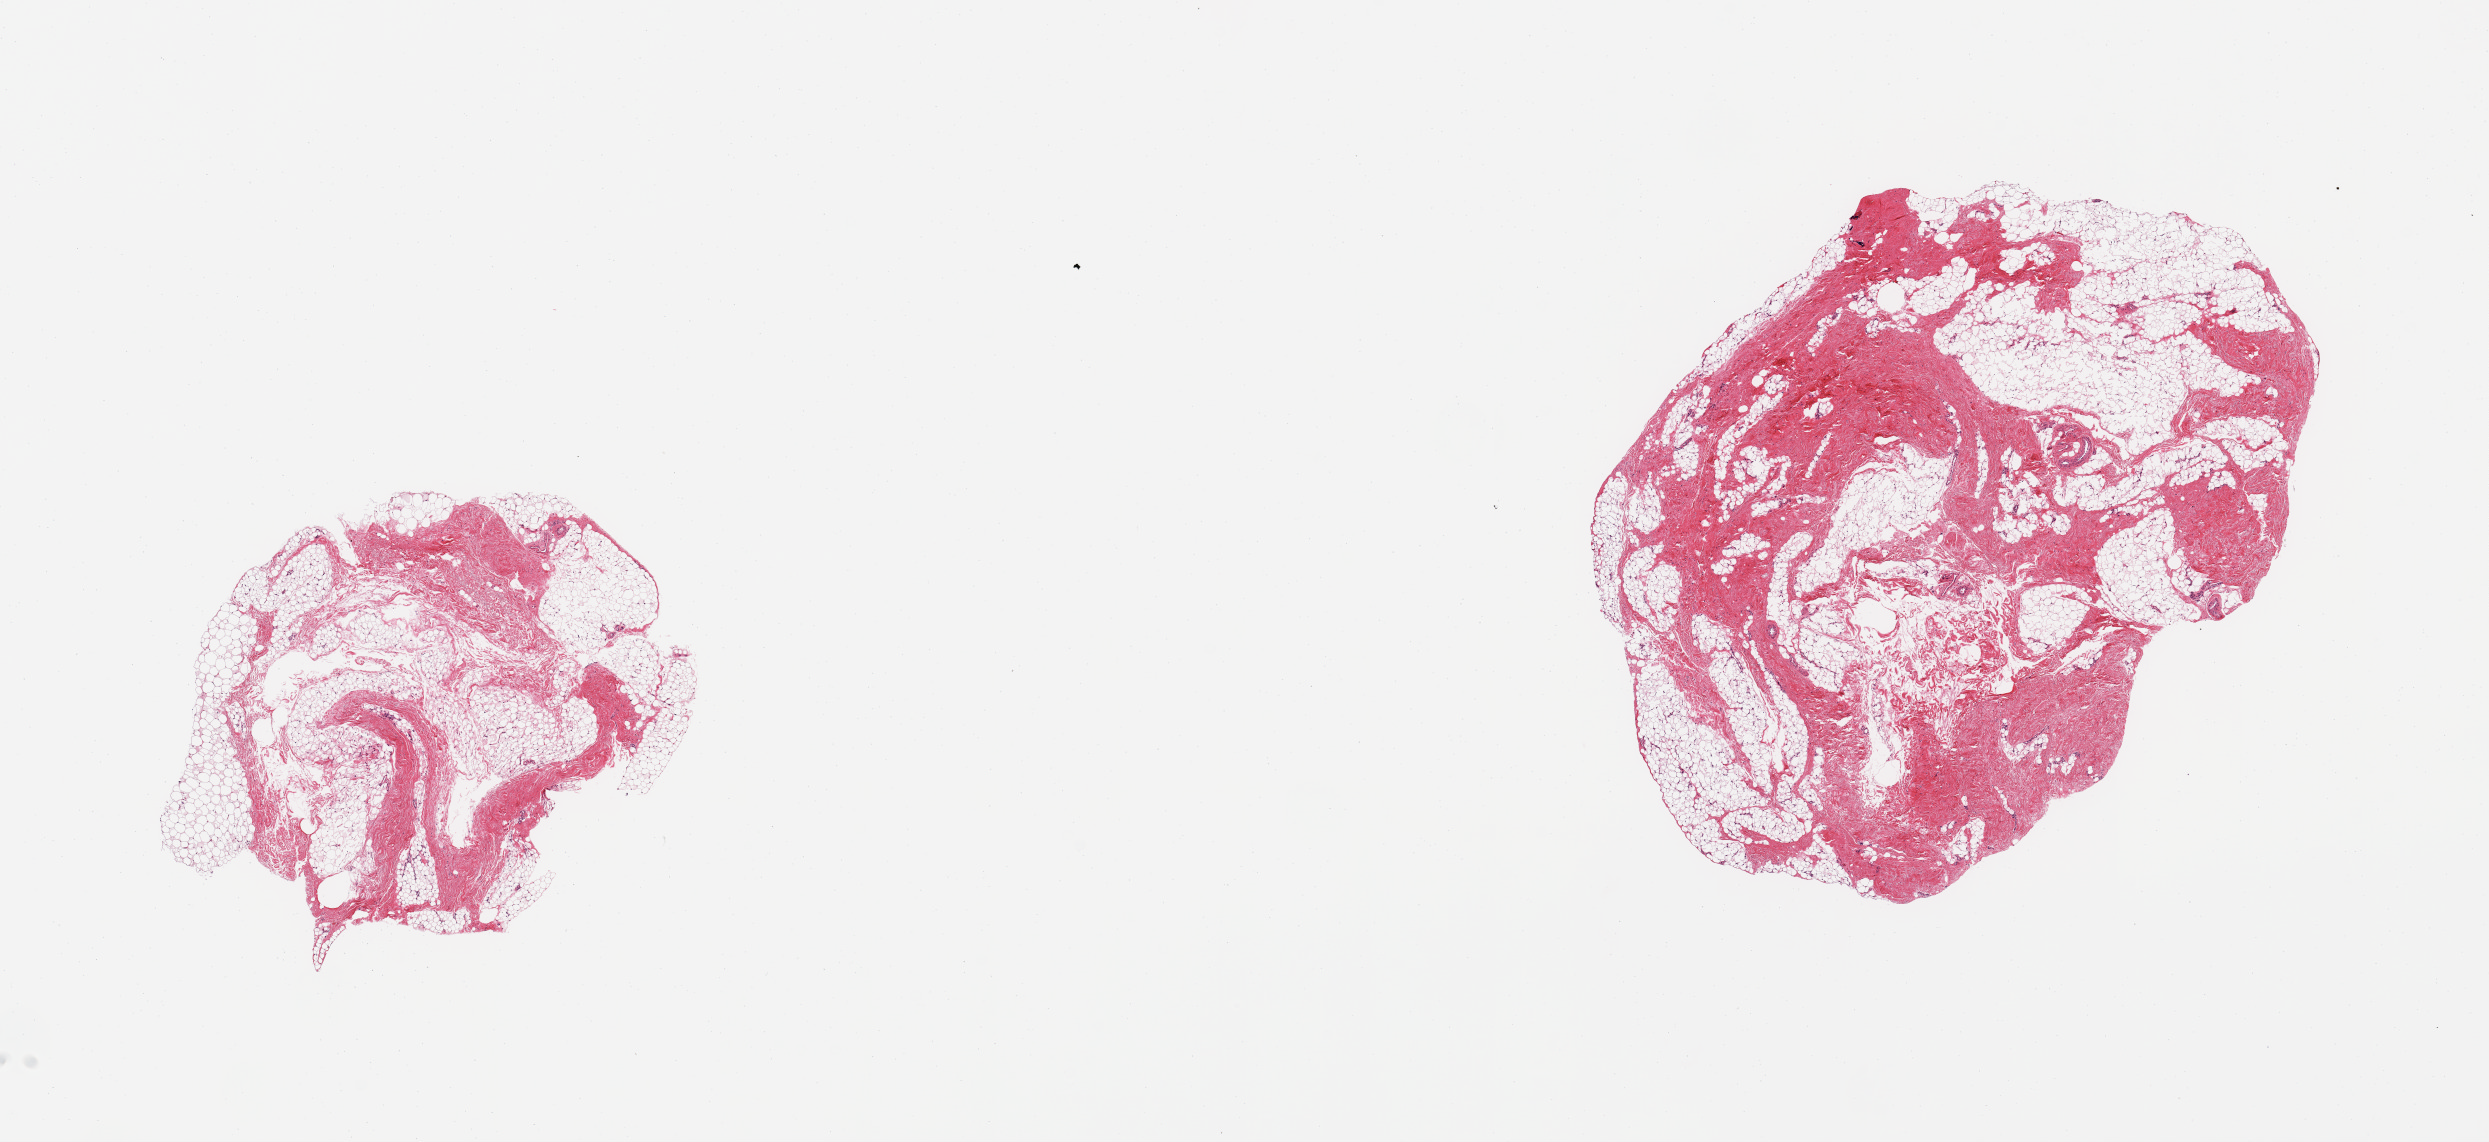
Whole-slide image, hematoxylin and eosin (H&E) stain, brightfield, shown as a low-resolution overview of the whole scanned area (about 19.7 x 9.0 mm, from a 20x scan); PAXgene-fixed paraffin-embedded (PFPE) section; section of breast (target tissue); donor tissue sample. Donor: male.
• pathologist's review note for this sample: 2 pieces; fibrofatty tissue with no obvious mammary ducts